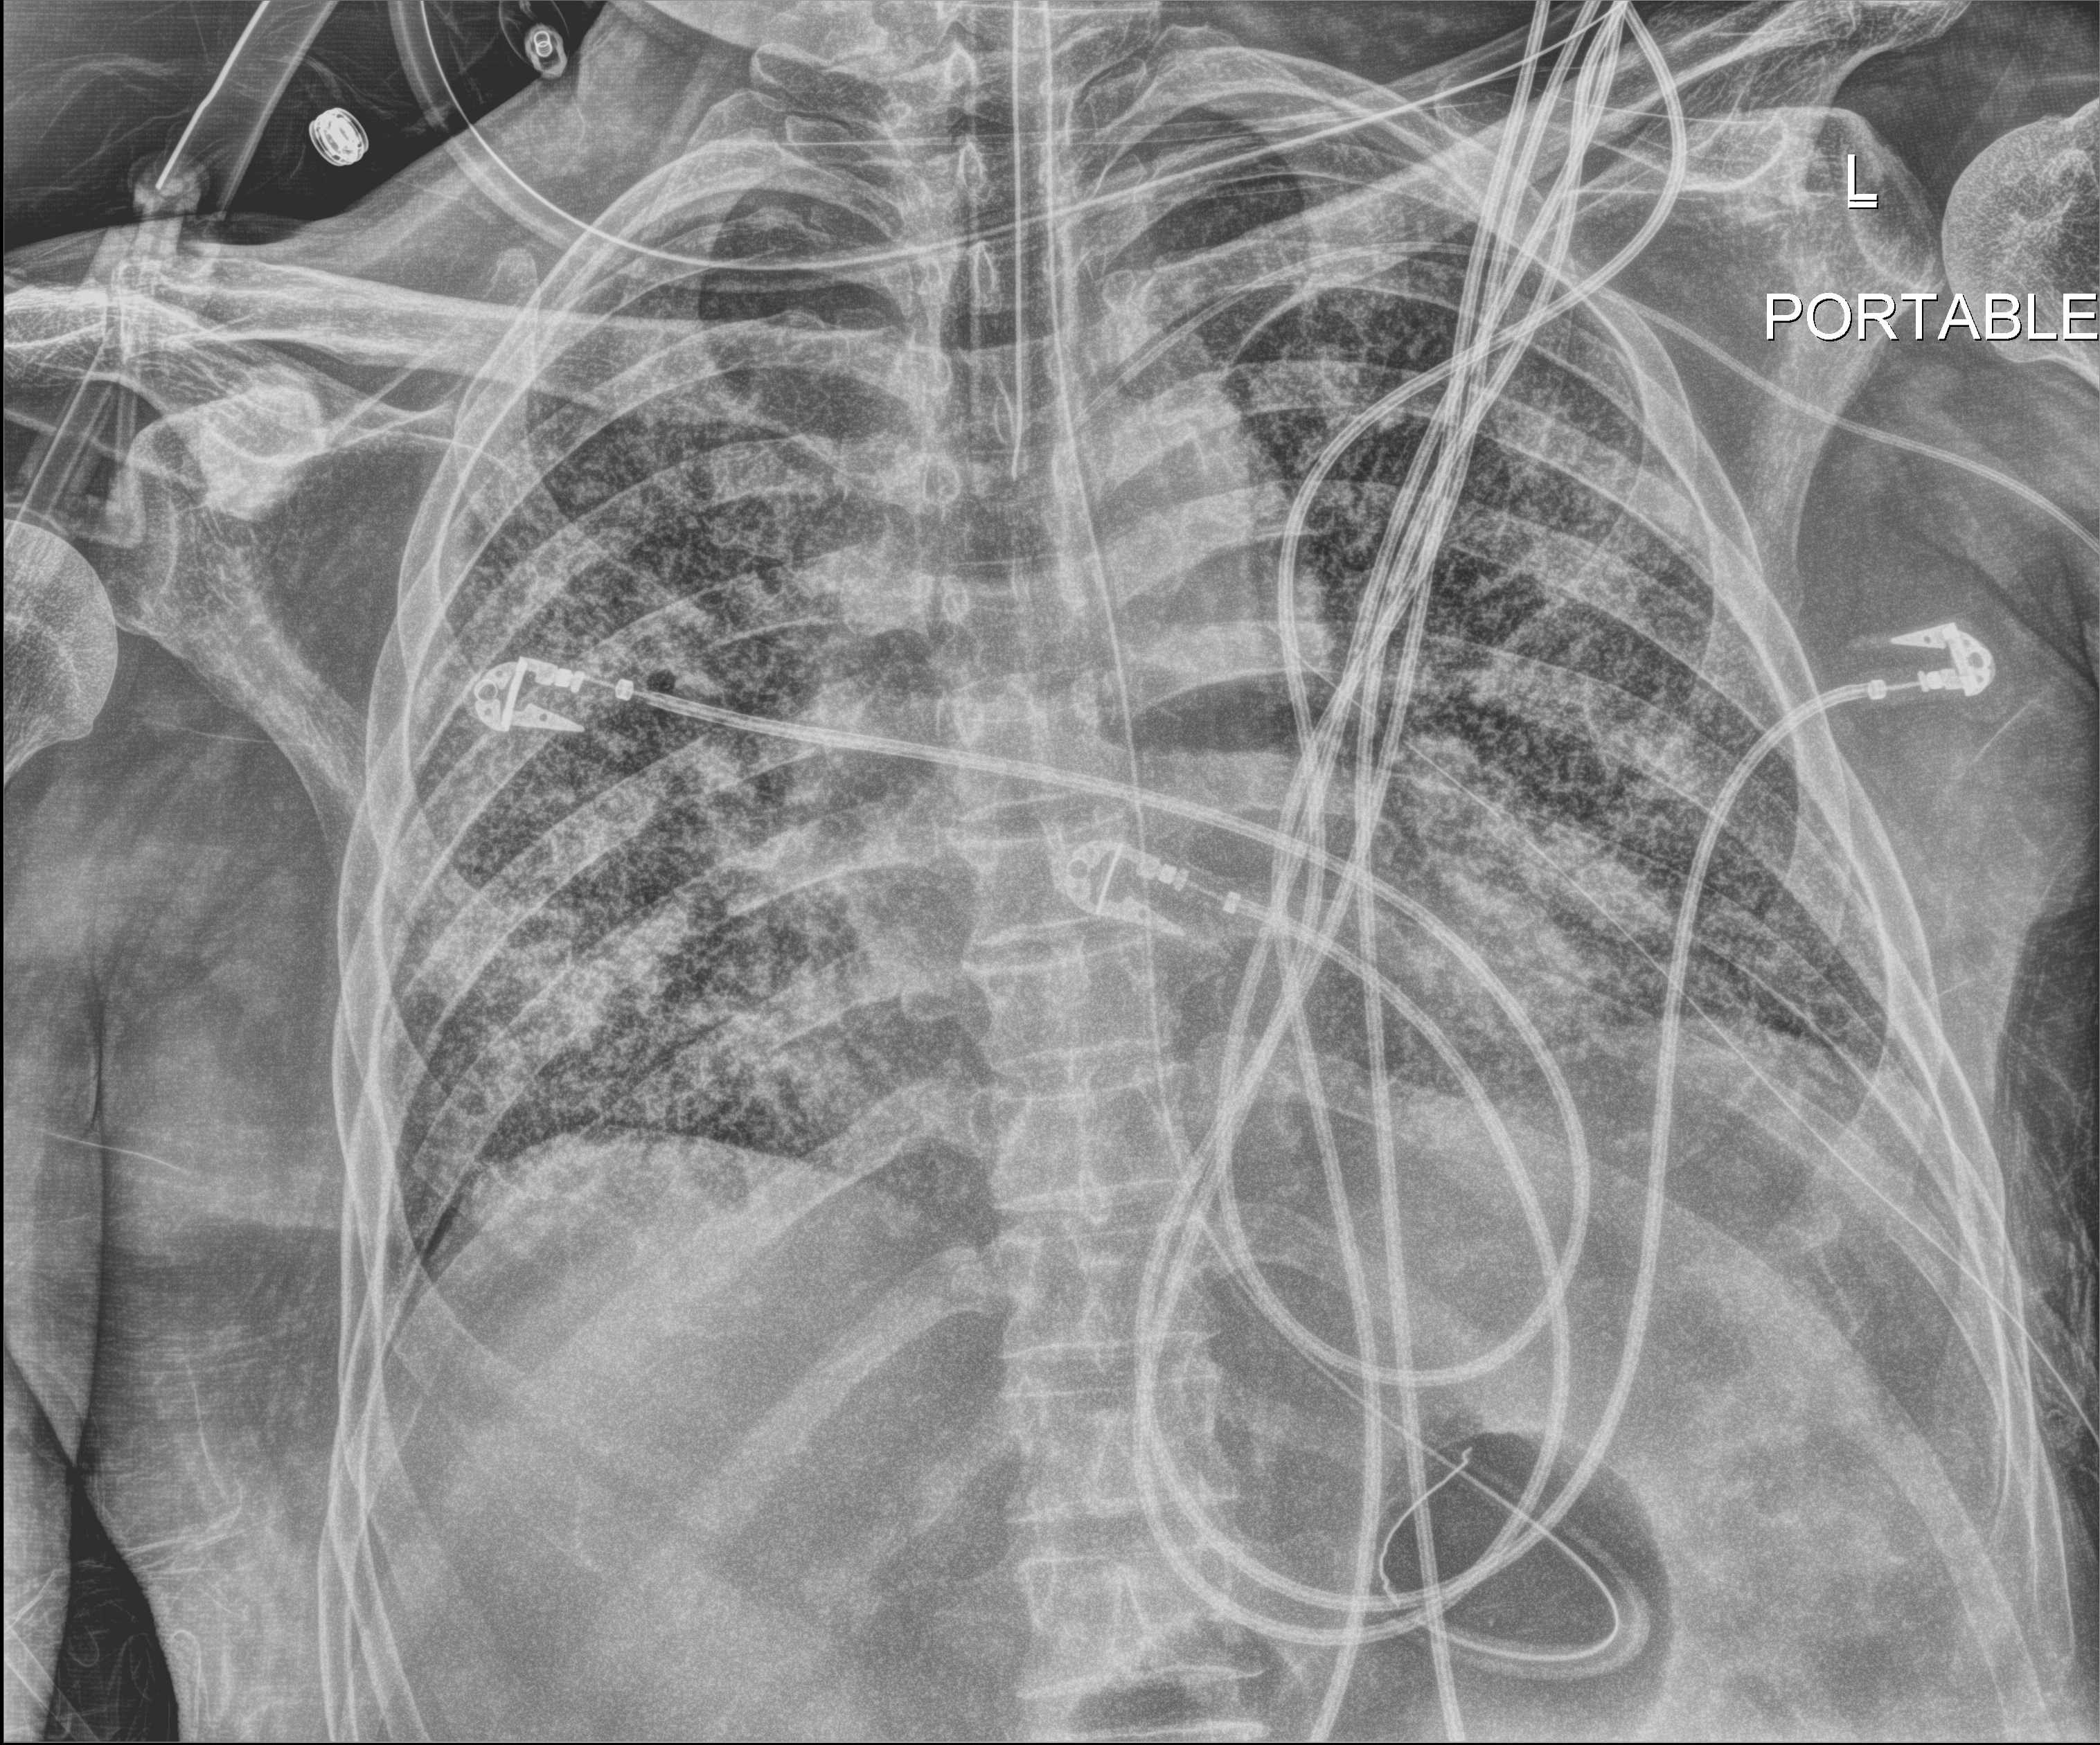
Bedside chest radiograph (digital radiography), anteroposterior (AP) projection. Male patient hospitalised with COVID-19, age 60–74 years.
Hospital-stay facts (about this admission, not read from this image; timing relative to this image not recorded): mechanically ventilated during this hospital stay: yes; admitted to intensive care during this hospital stay: yes.